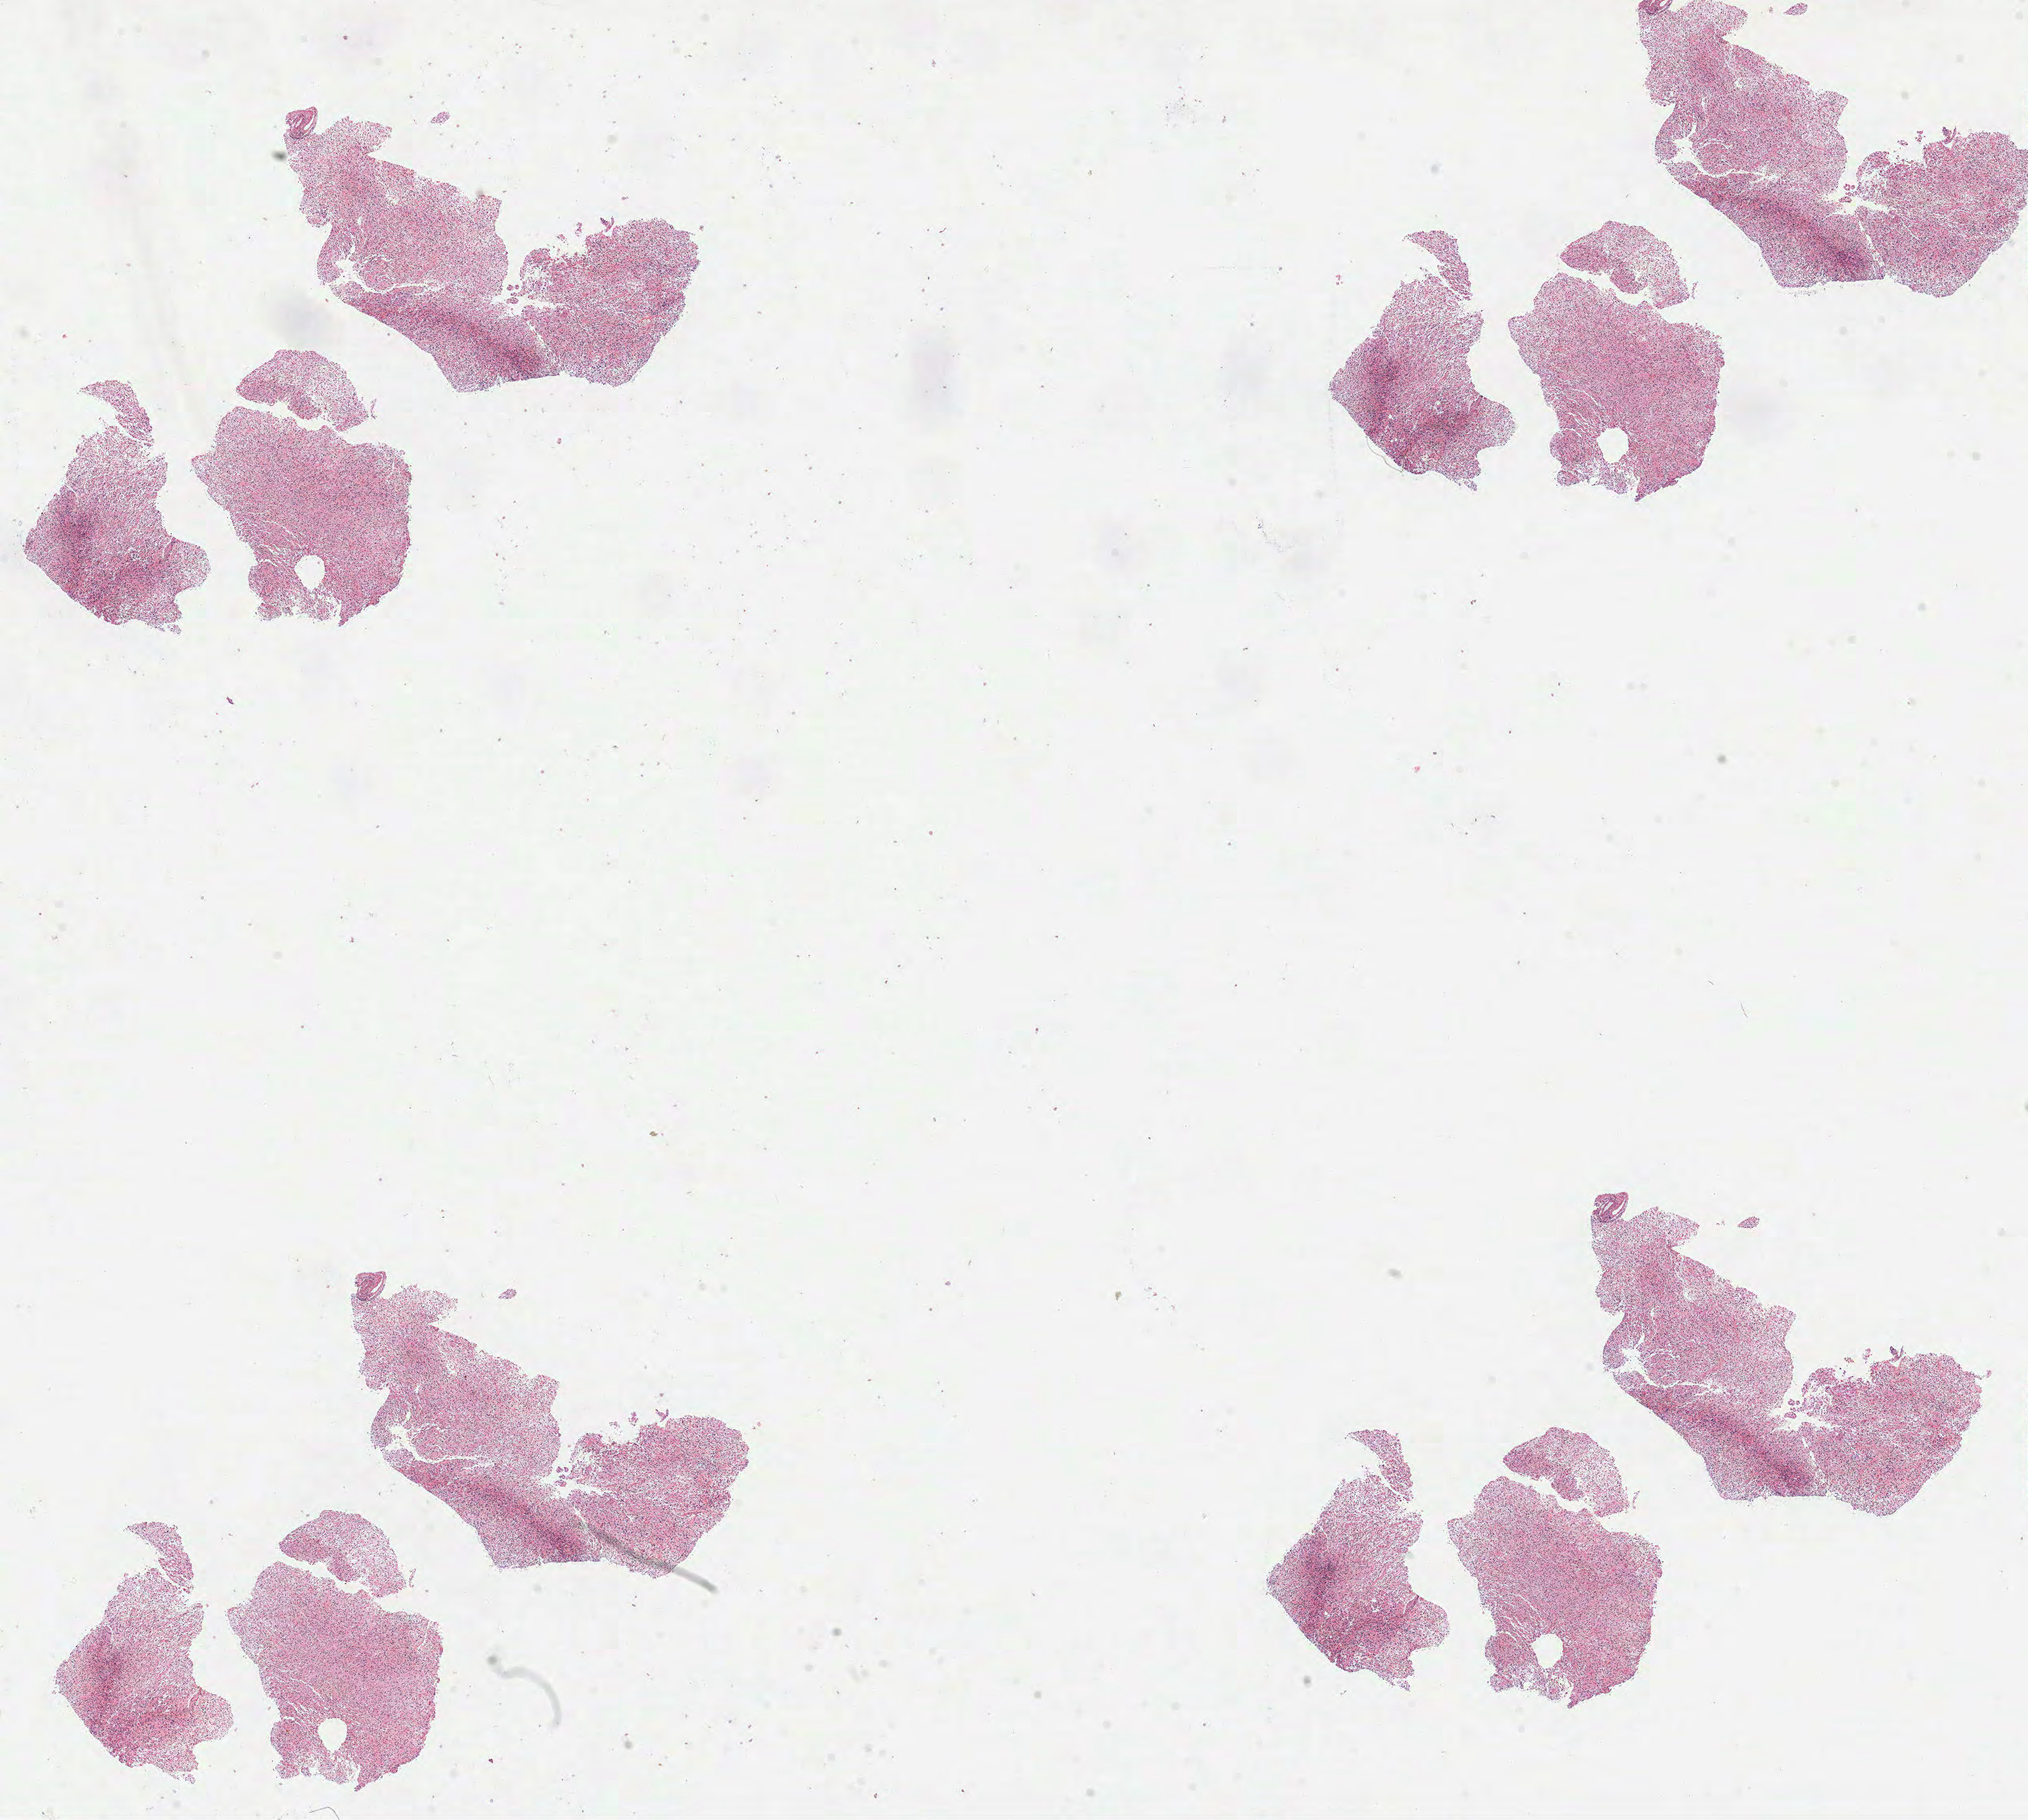
Hematoxylin and eosin (H&E) stained whole-slide image, low-resolution overview of the scanned area, about 20.3 x 18.2 mm (acquisition: 40x scan), formalin-fixed paraffin-embedded (FFPE) diagnostic section, sample: primary tumour, brain. Female patient; age at initial diagnosis 31 years. Histologic grade: G3 (poorly differentiated).
Histologic diagnosis: Mixed glioma (cerebrum).